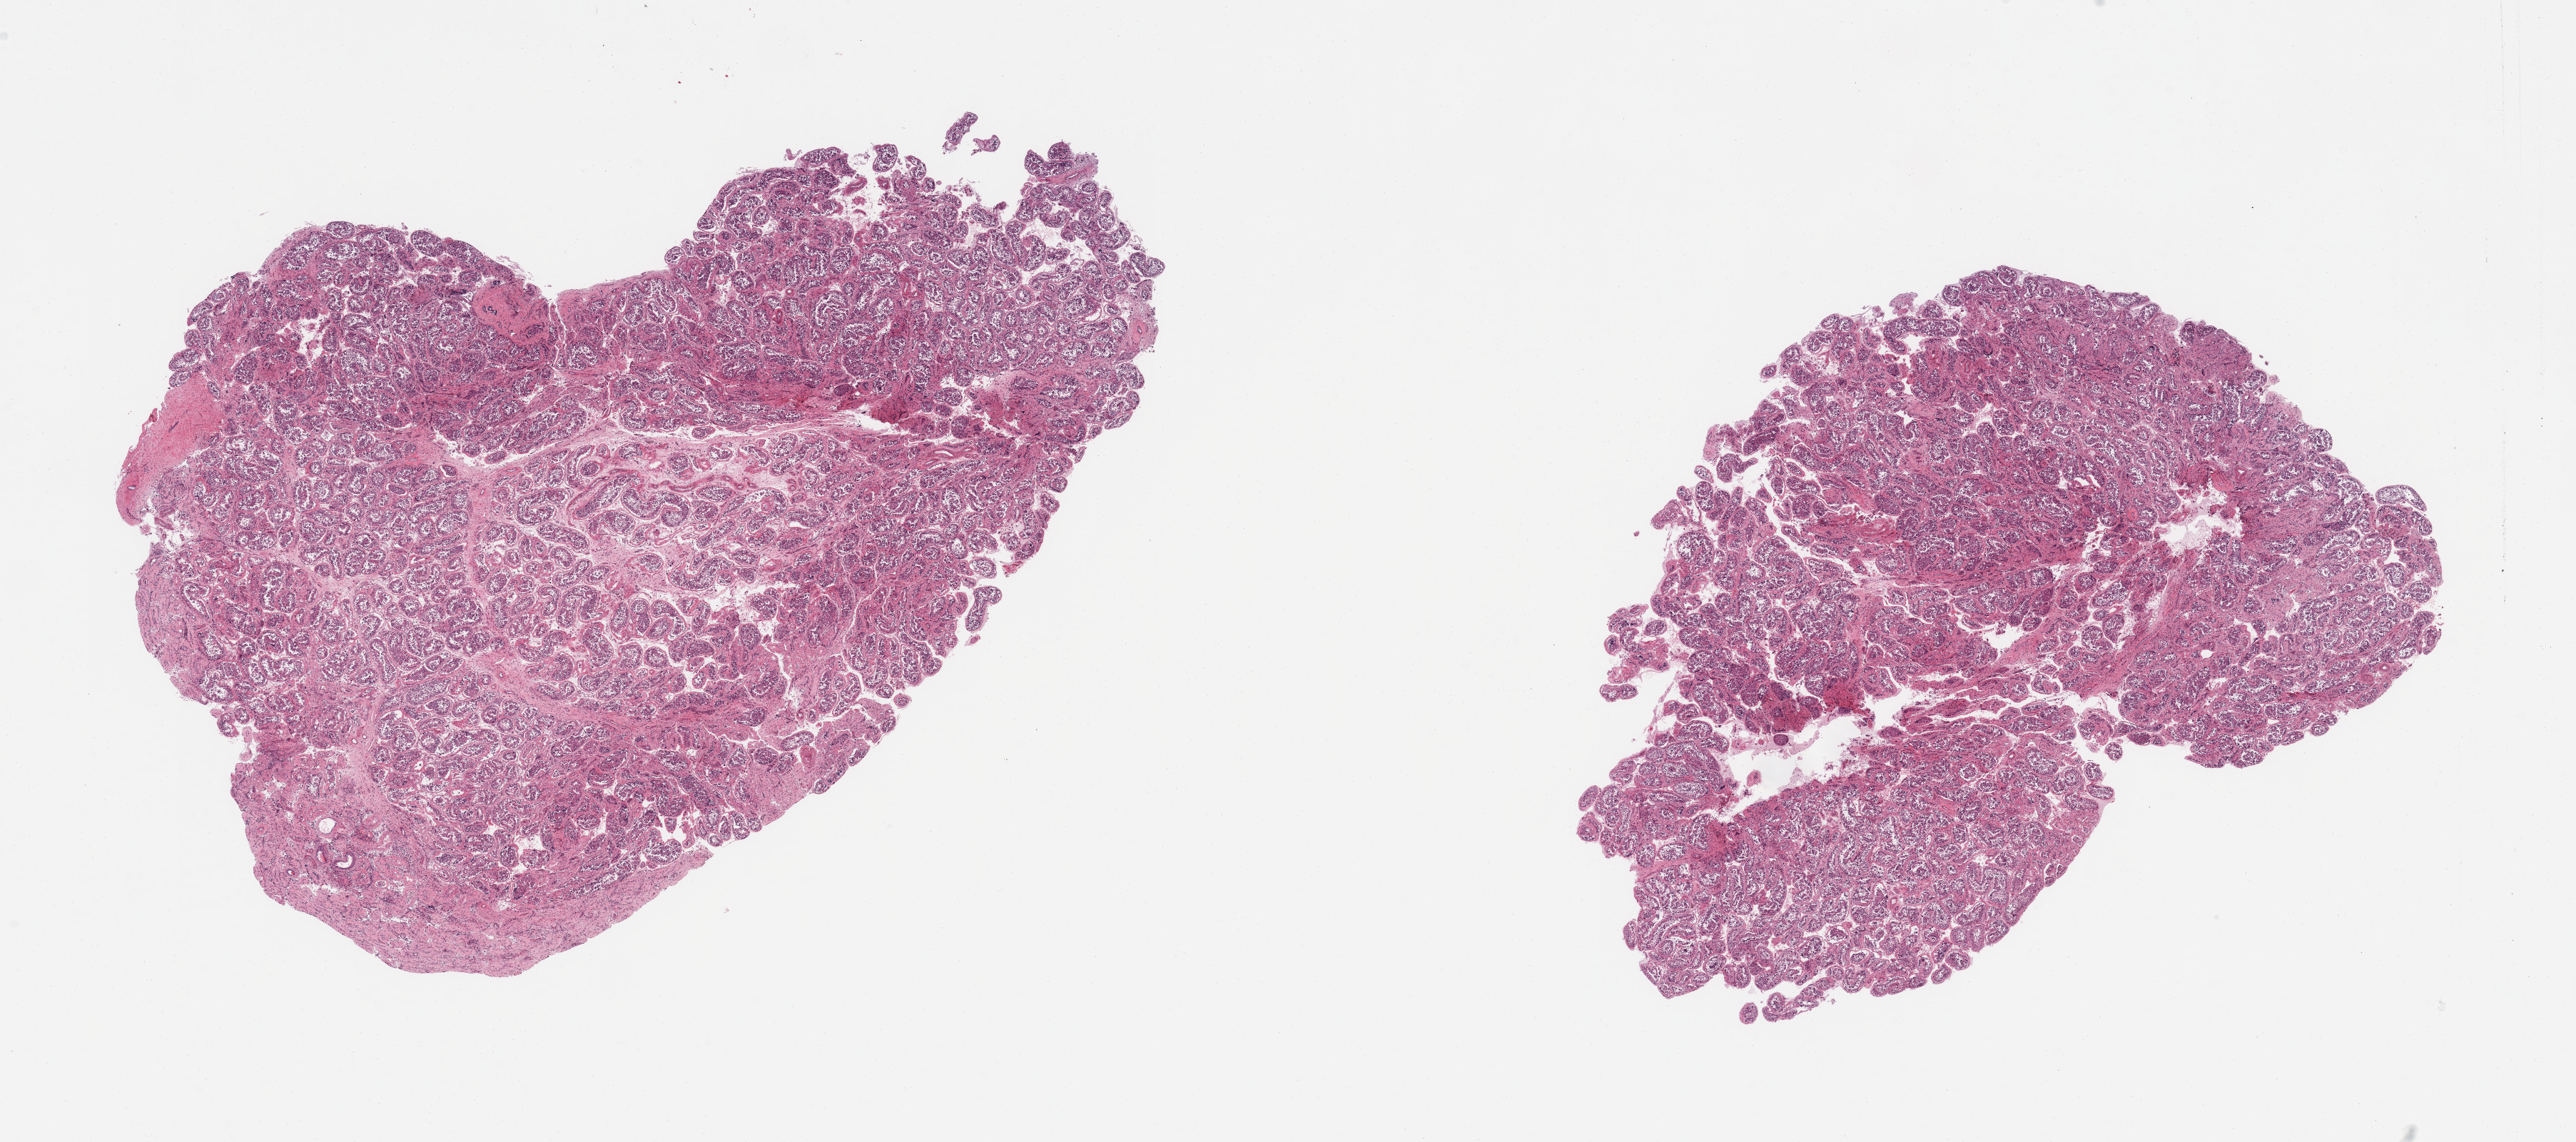
Digitized H&E-stained section, brightfield, shown as a low-resolution overview of the whole scanned area (about 28.5 x 12.7 mm). PAXgene-fixed paraffin-embedded (PFPE) section. Target tissue: testis. Tissue donor sample. Donor: male.
Pathologist's review note for this sample: 2 pieces, moderately autolyzed; spermatogenesis appears reduced.